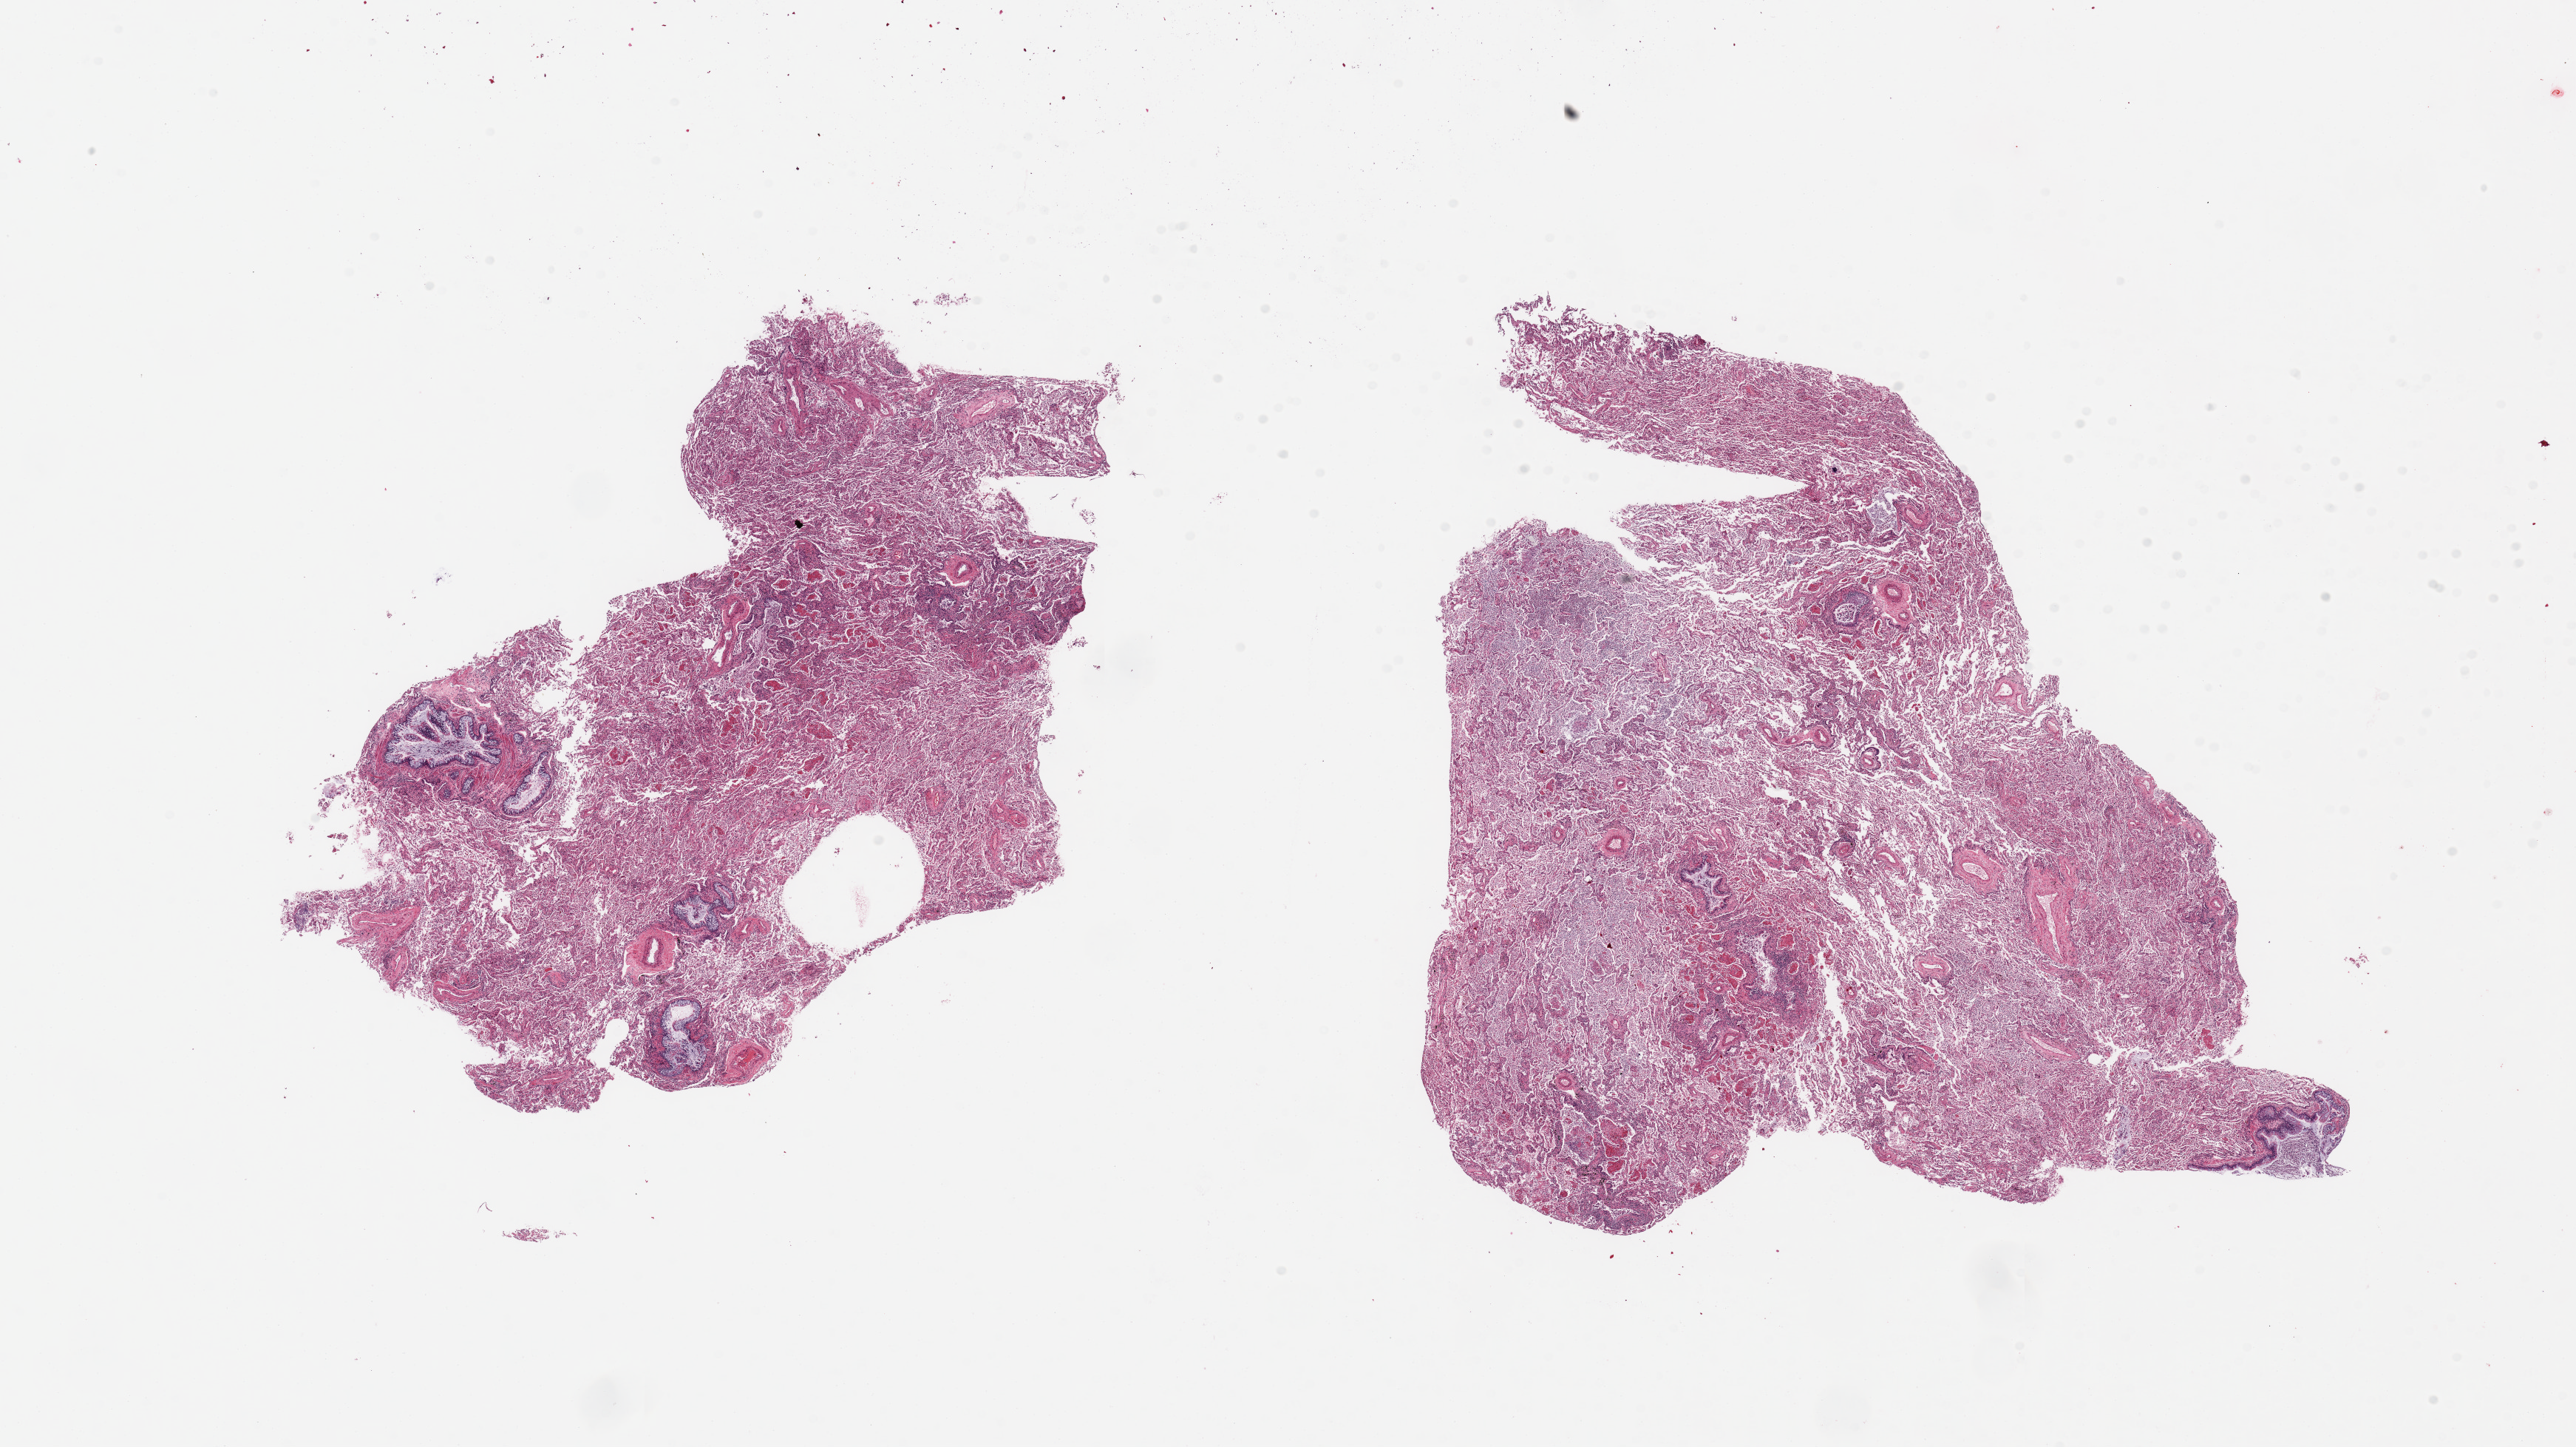
Whole-slide image, haematoxylin and eosin stain — whole scanned area (about 27.6 x 15.5 mm) shown as a low-resolution overview, PAXgene-fixed, paraffin-embedded tissue, target tissue: lung, donor tissue sample. Donor: male.
Reviewer comment on this tissue sample: 2 pieces; organizing bronchopneumonia, bronchial smooth muscle hypertrophy and increased mucosal goblet cells (suggestive of asthma).